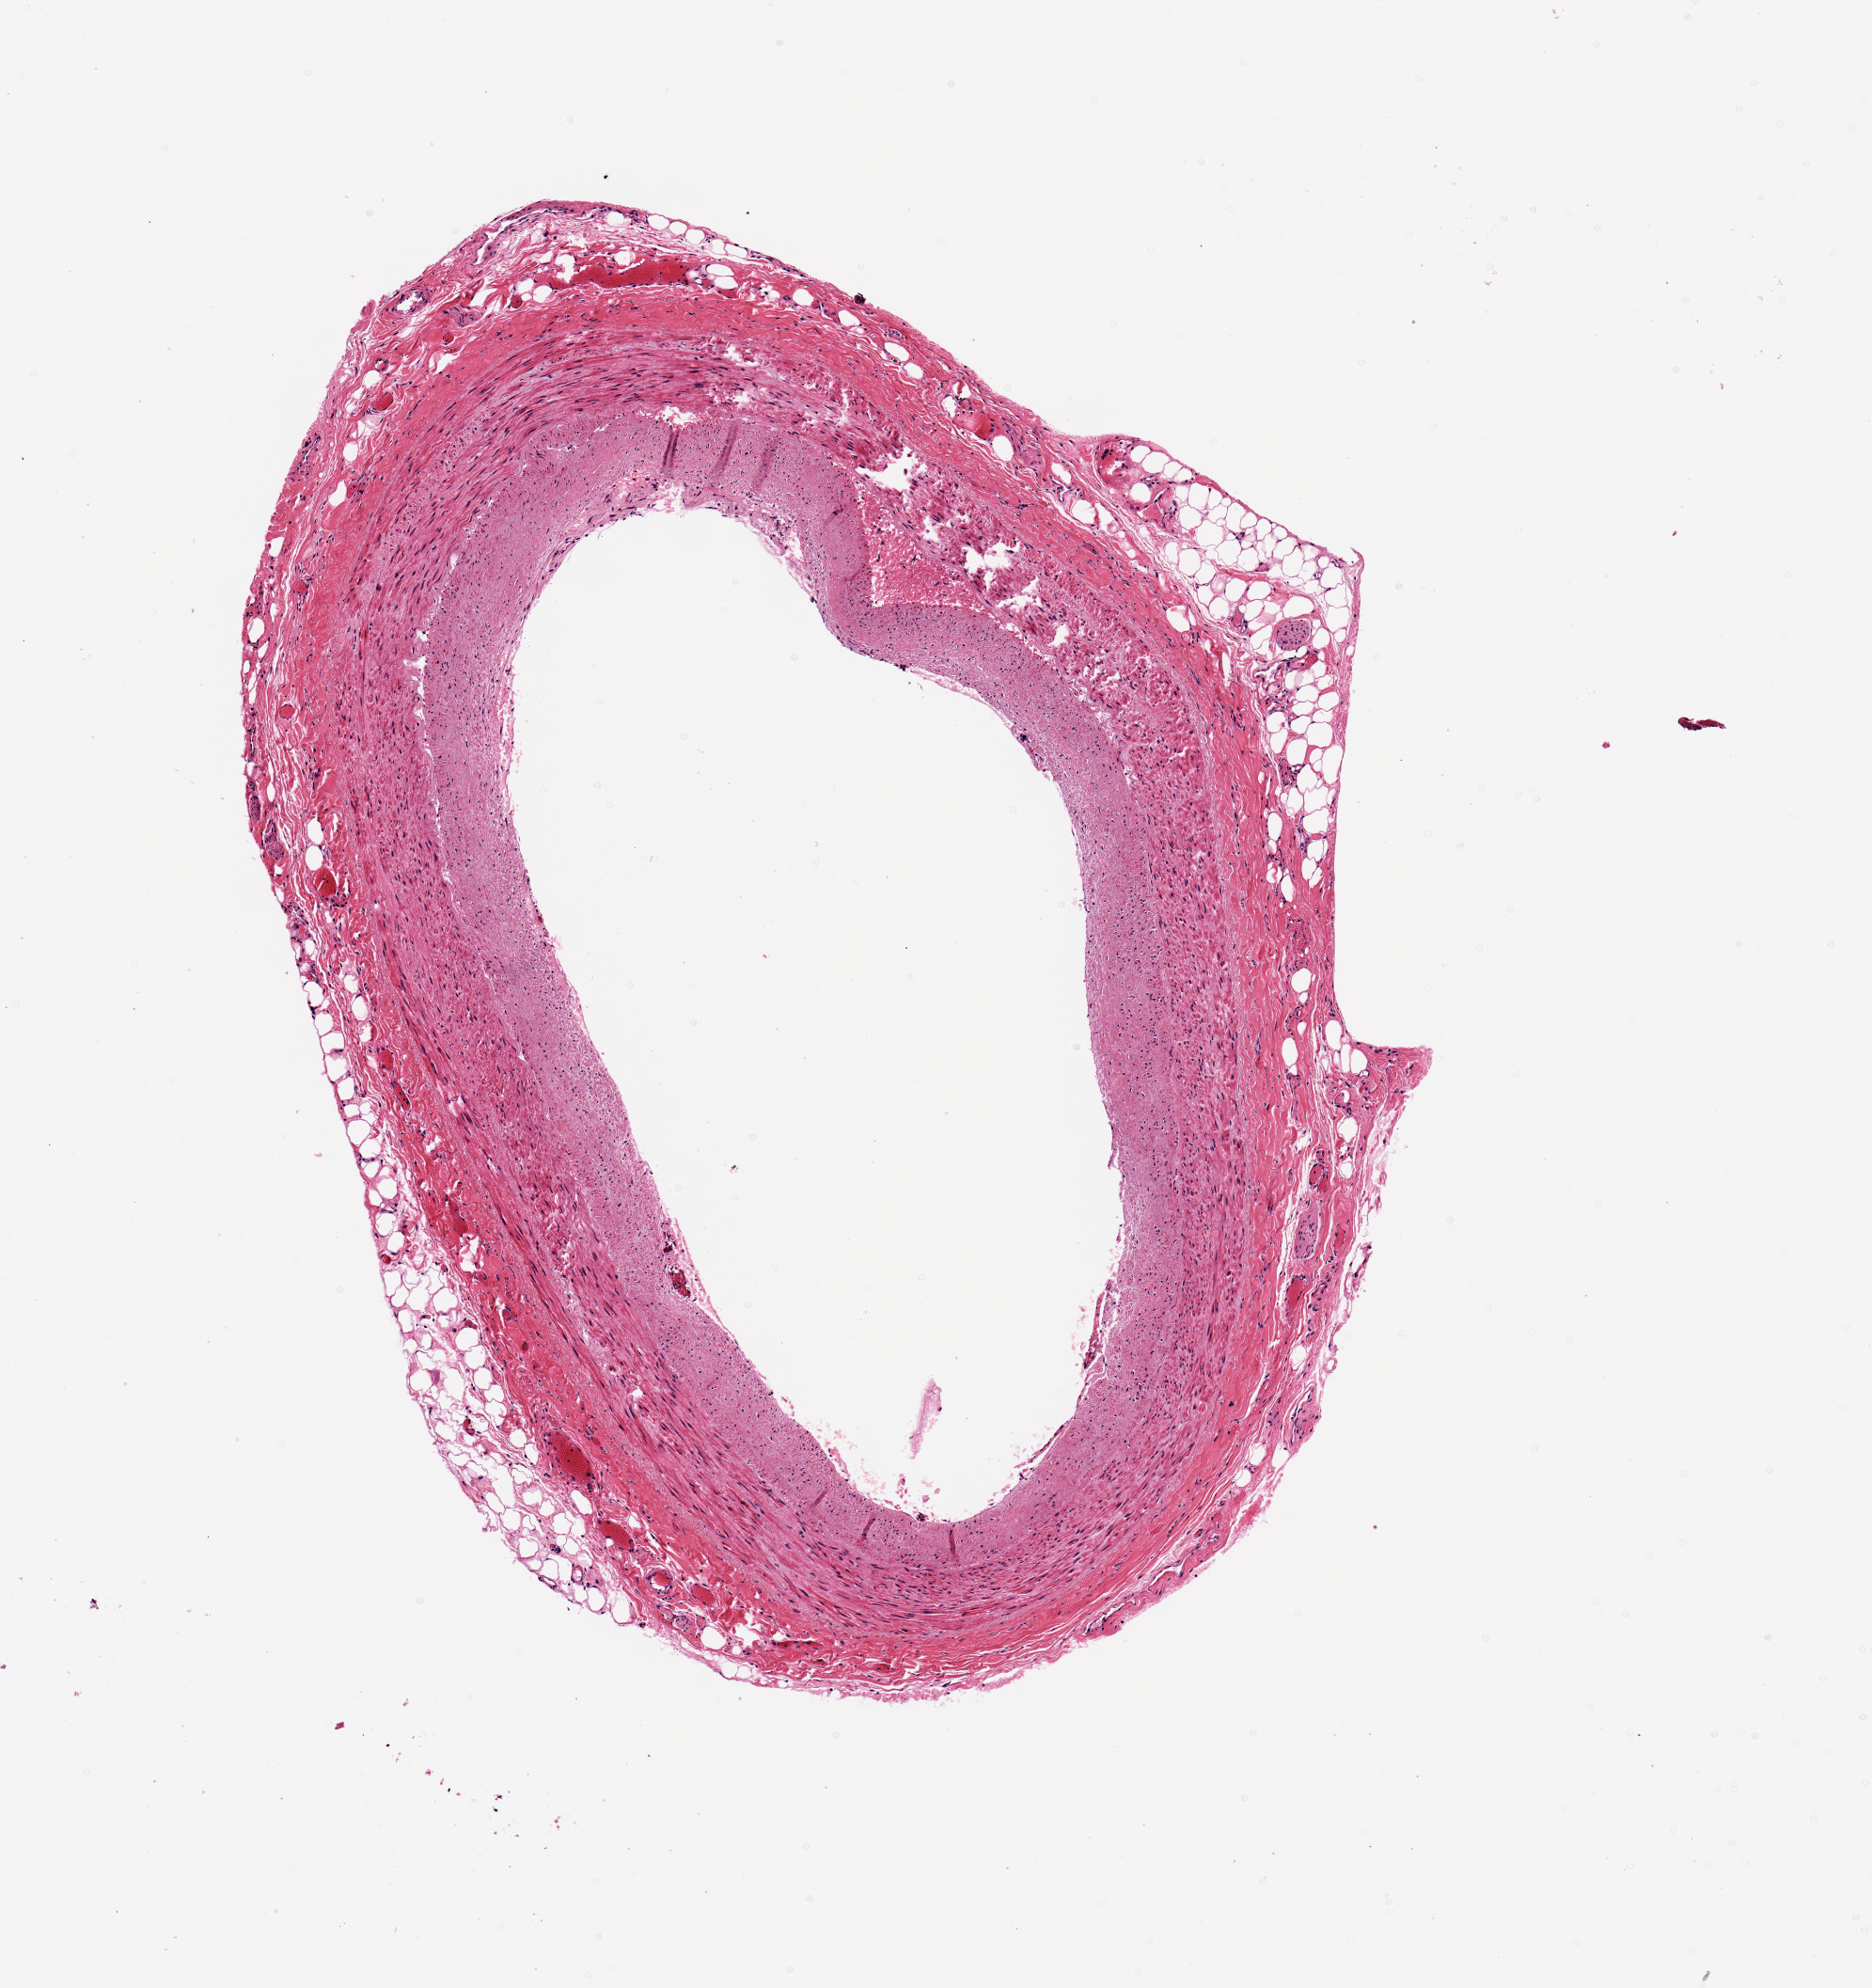
Digitized H&E-stained section, whole scanned area (about 3.9 x 4.2 mm, slide scanned at 20x) shown as a low-resolution overview. PAXgene-fixed, paraffin-embedded tissue. Section of coronary artery (target tissue). Tissue donor sample. Female donor.
• pathologist's review note for this sample: 2 x 3mm clean specimen; no atherosclerosis